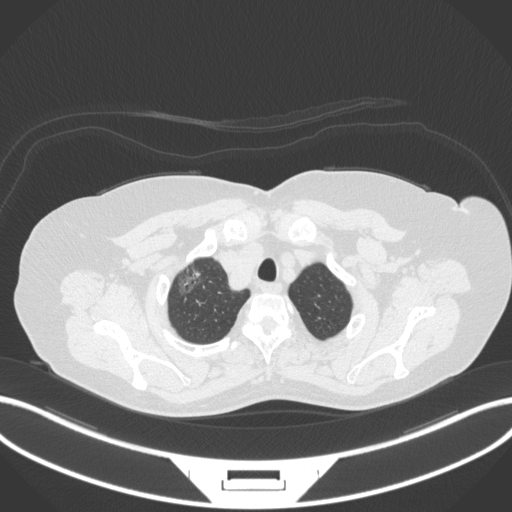
Chest CT, one axial slice. Slice 313 of 365 in the series (ordered by position). 120 kVp. Lung window (W 1500 / L -600 HU). 1 mm slice thickness. 512 × 512 image matrix, field of view 400 × 400 mm. Patient: female, 62 years. From the clinical record (not read from this slice): clinical TNM (as recorded): T1c N0 M0.
Outlined on this slice (bounding box drawn by a radiologist):
- lung tumour (recorded histology: adenocarcinoma): bounding box [x1, y1, x2, y2] px = [173, 256, 208, 298]